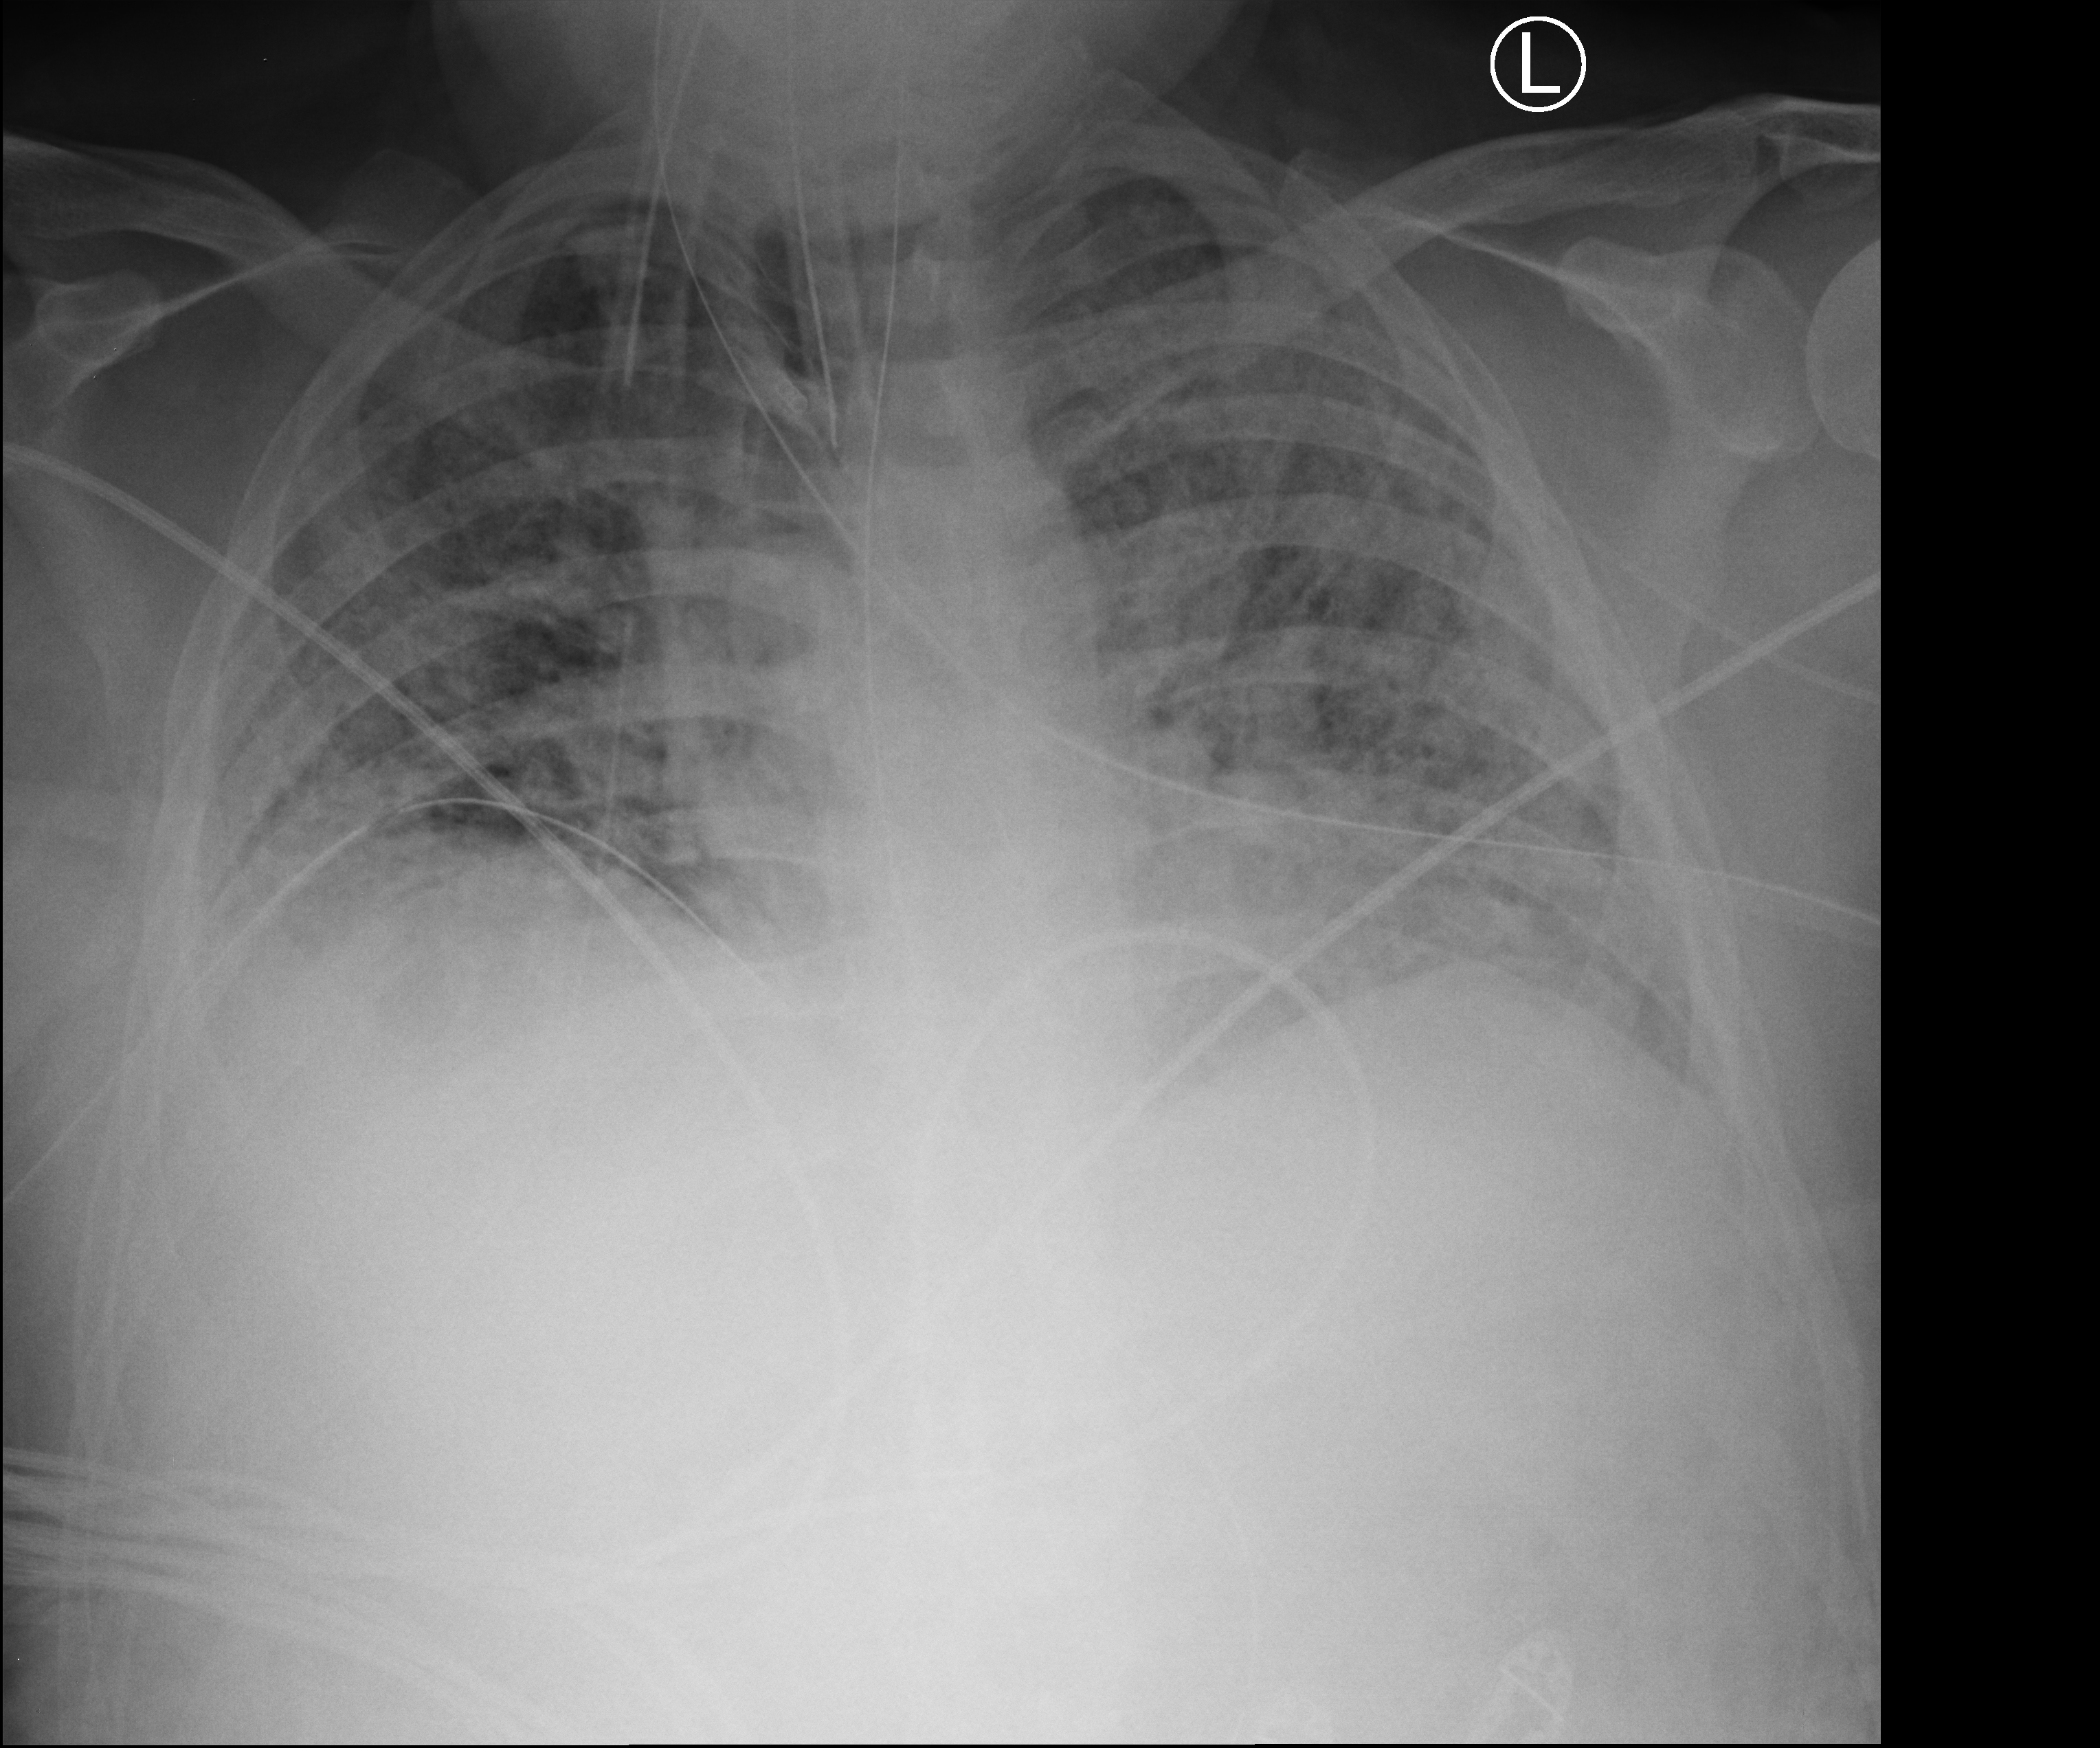
Portable chest radiograph; anteroposterior (AP) projection. Patient hospitalised with COVID-19; male, aged 18–59 years.
Hospital-stay facts (about this admission, not read from this image; timing relative to this image not recorded):
- length of hospital stay: 80 days
- mechanically ventilated during this hospital stay: yes